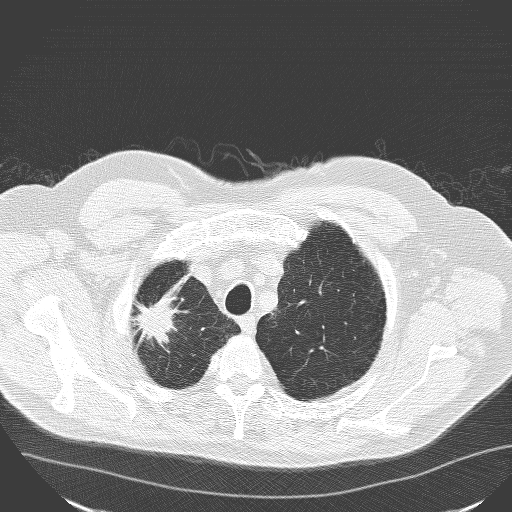
Low-dose screening chest CT, one axial slice. Slice 140 of 160 in the series (ordered by position). 120 kVp. Lung window (W 1500 / L -600 HU). 3.2 mm slice thickness. 512 × 512 image matrix.
Annotated regions visible in this slice (manually delineated by an expert):
- lesion 1 (tumor, upper lobe of right lung): bounding box [x1, y1, x2, y2] px = [139, 301, 174, 344]